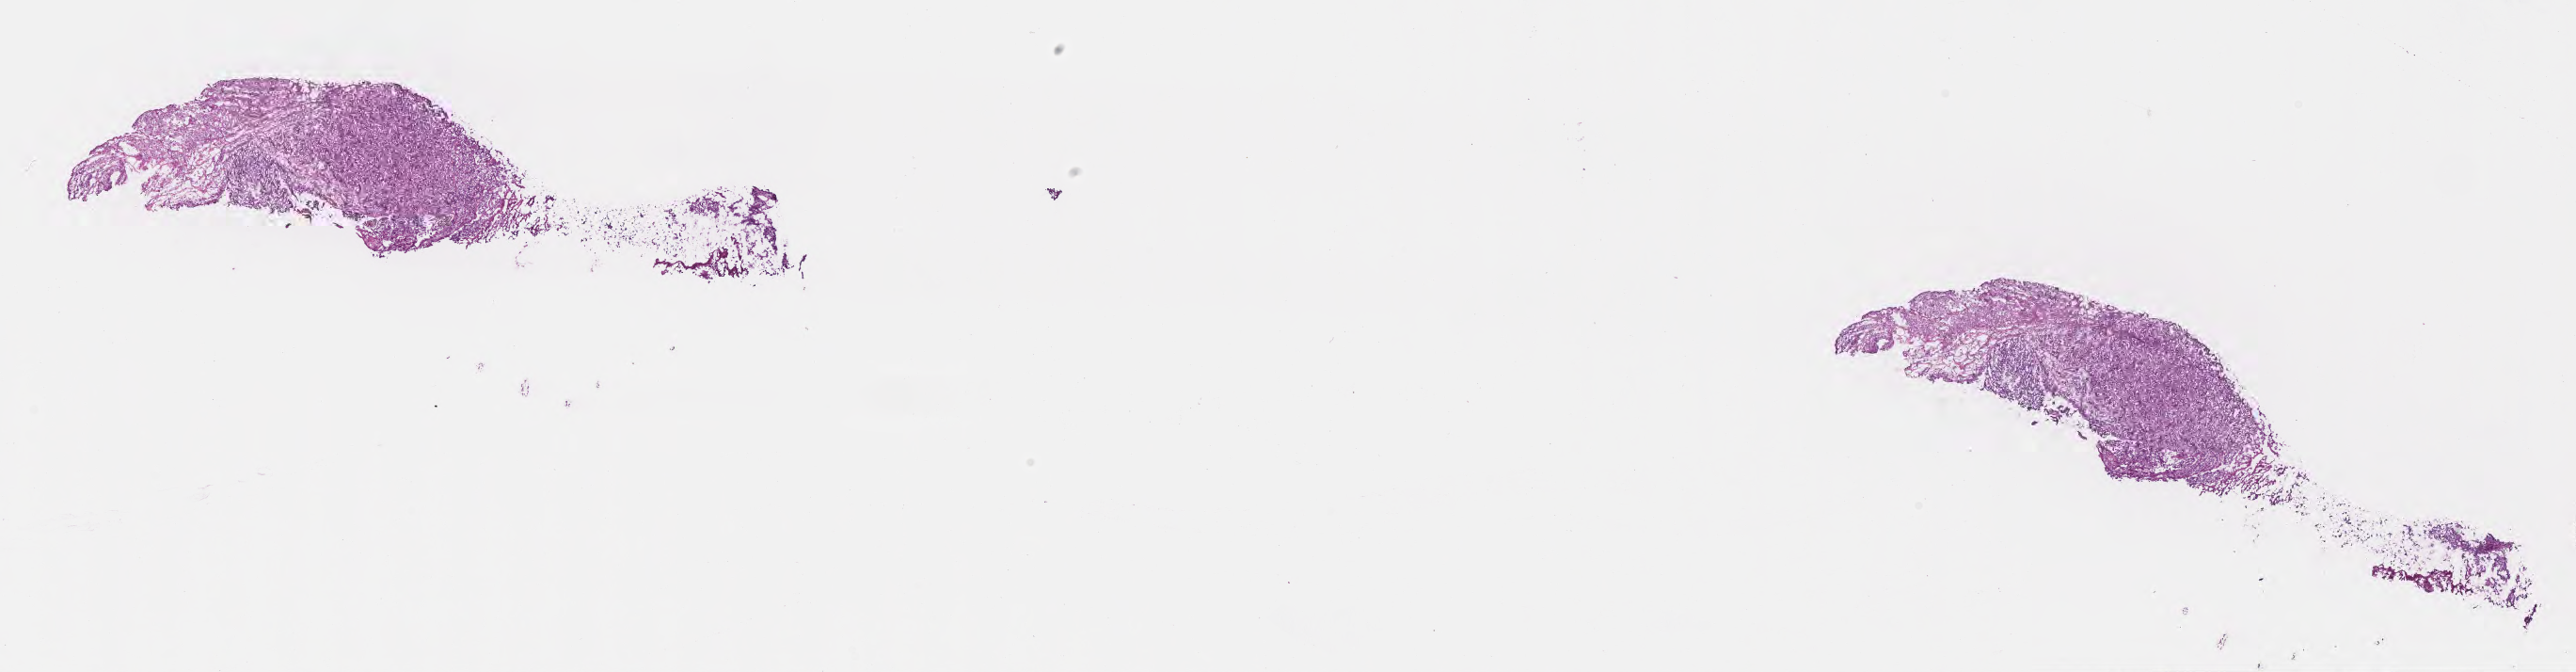
Digitized hematoxylin and eosin (H&E)-stained section, whole scanned area (about 22.1 x 5.8 mm) shown as a low-resolution overview; frozen section (snap frozen); specimen: metastatic tumor tissue, resected from brain. Male, age 48 years at initial diagnosis. Pathologist review of this section (percent, as recorded): tumor cells 75%, tumor nuclei 75%, stromal cells 24%, necrosis 1%, normal cells 0%. Infiltration values recorded for this section: lymphocyte infiltration 3%, monocyte infiltration 4%, neutrophil infiltration 5%.
• patient diagnosis (primary): Carcinoma, NOS